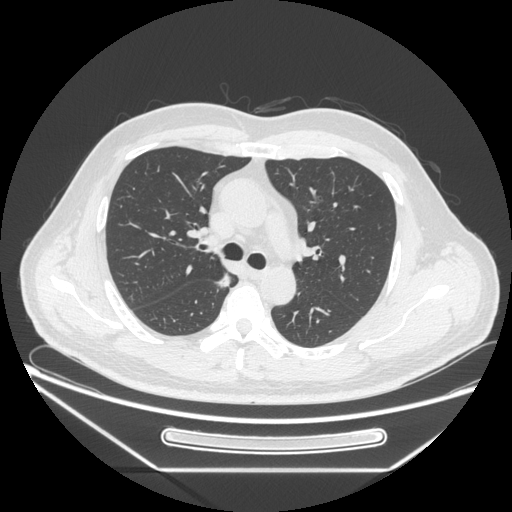
Chest CT, one axial slice; slice 166 of 271 in the series (ordered by position); lung window (W 1500 / L -600 HU); 512 × 512 image matrix, field of view 414 × 414 mm. Patient: male, 49 years. From the clinical record (not read from this slice): clinical TNM (as recorded): T1b N0 M0; histopathological grade: G2.
Annotated regions visible in this slice (bounding box drawn by a radiologist):
- lung tumour (recorded histology: adenocarcinoma): bounding box [x1, y1, x2, y2] px = [215, 270, 231, 292]